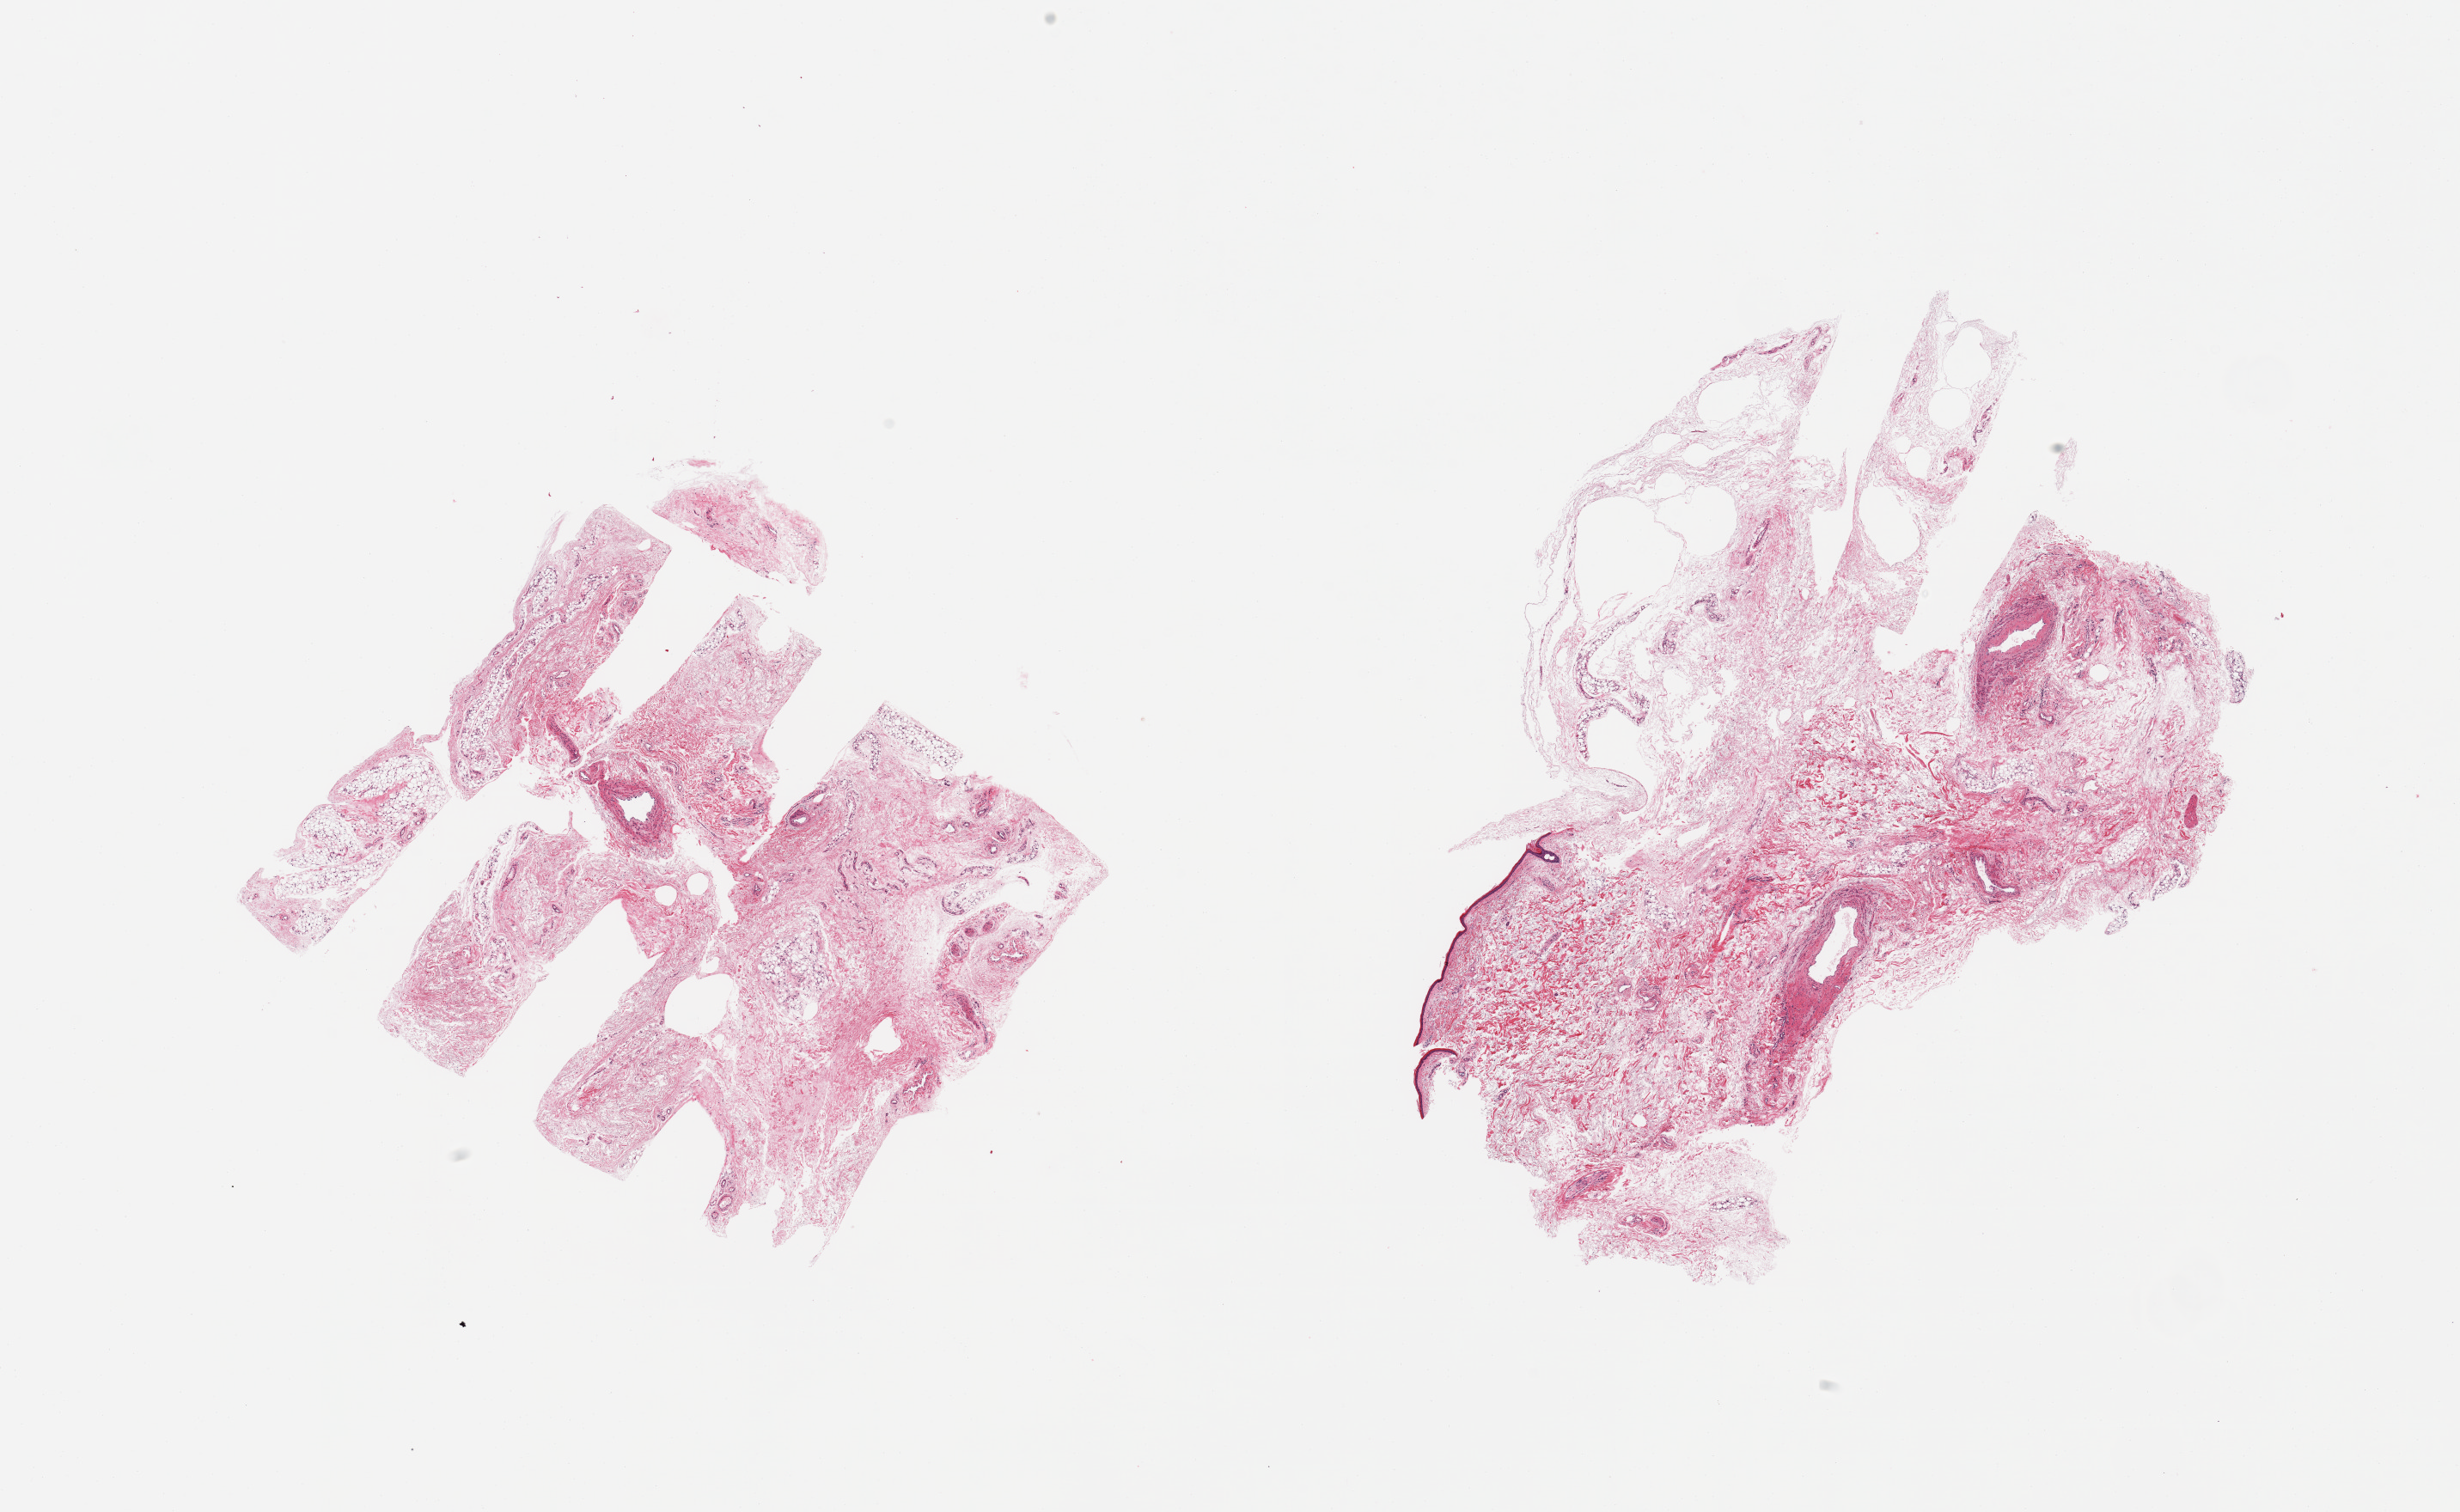
Whole-slide image, hematoxylin and eosin (H&E) stain, brightfield, whole scanned area (about 22.6 x 13.9 mm) shown as a low-resolution overview. PAXgene-fixed paraffin-embedded (PFPE) section. Section of adipose tissue (target tissue). Donor tissue sample. Male donor.
Pathologist's review note for this sample: 2 pieces; atrophic with 30% diffuse fibrous content; 3mm of skin.